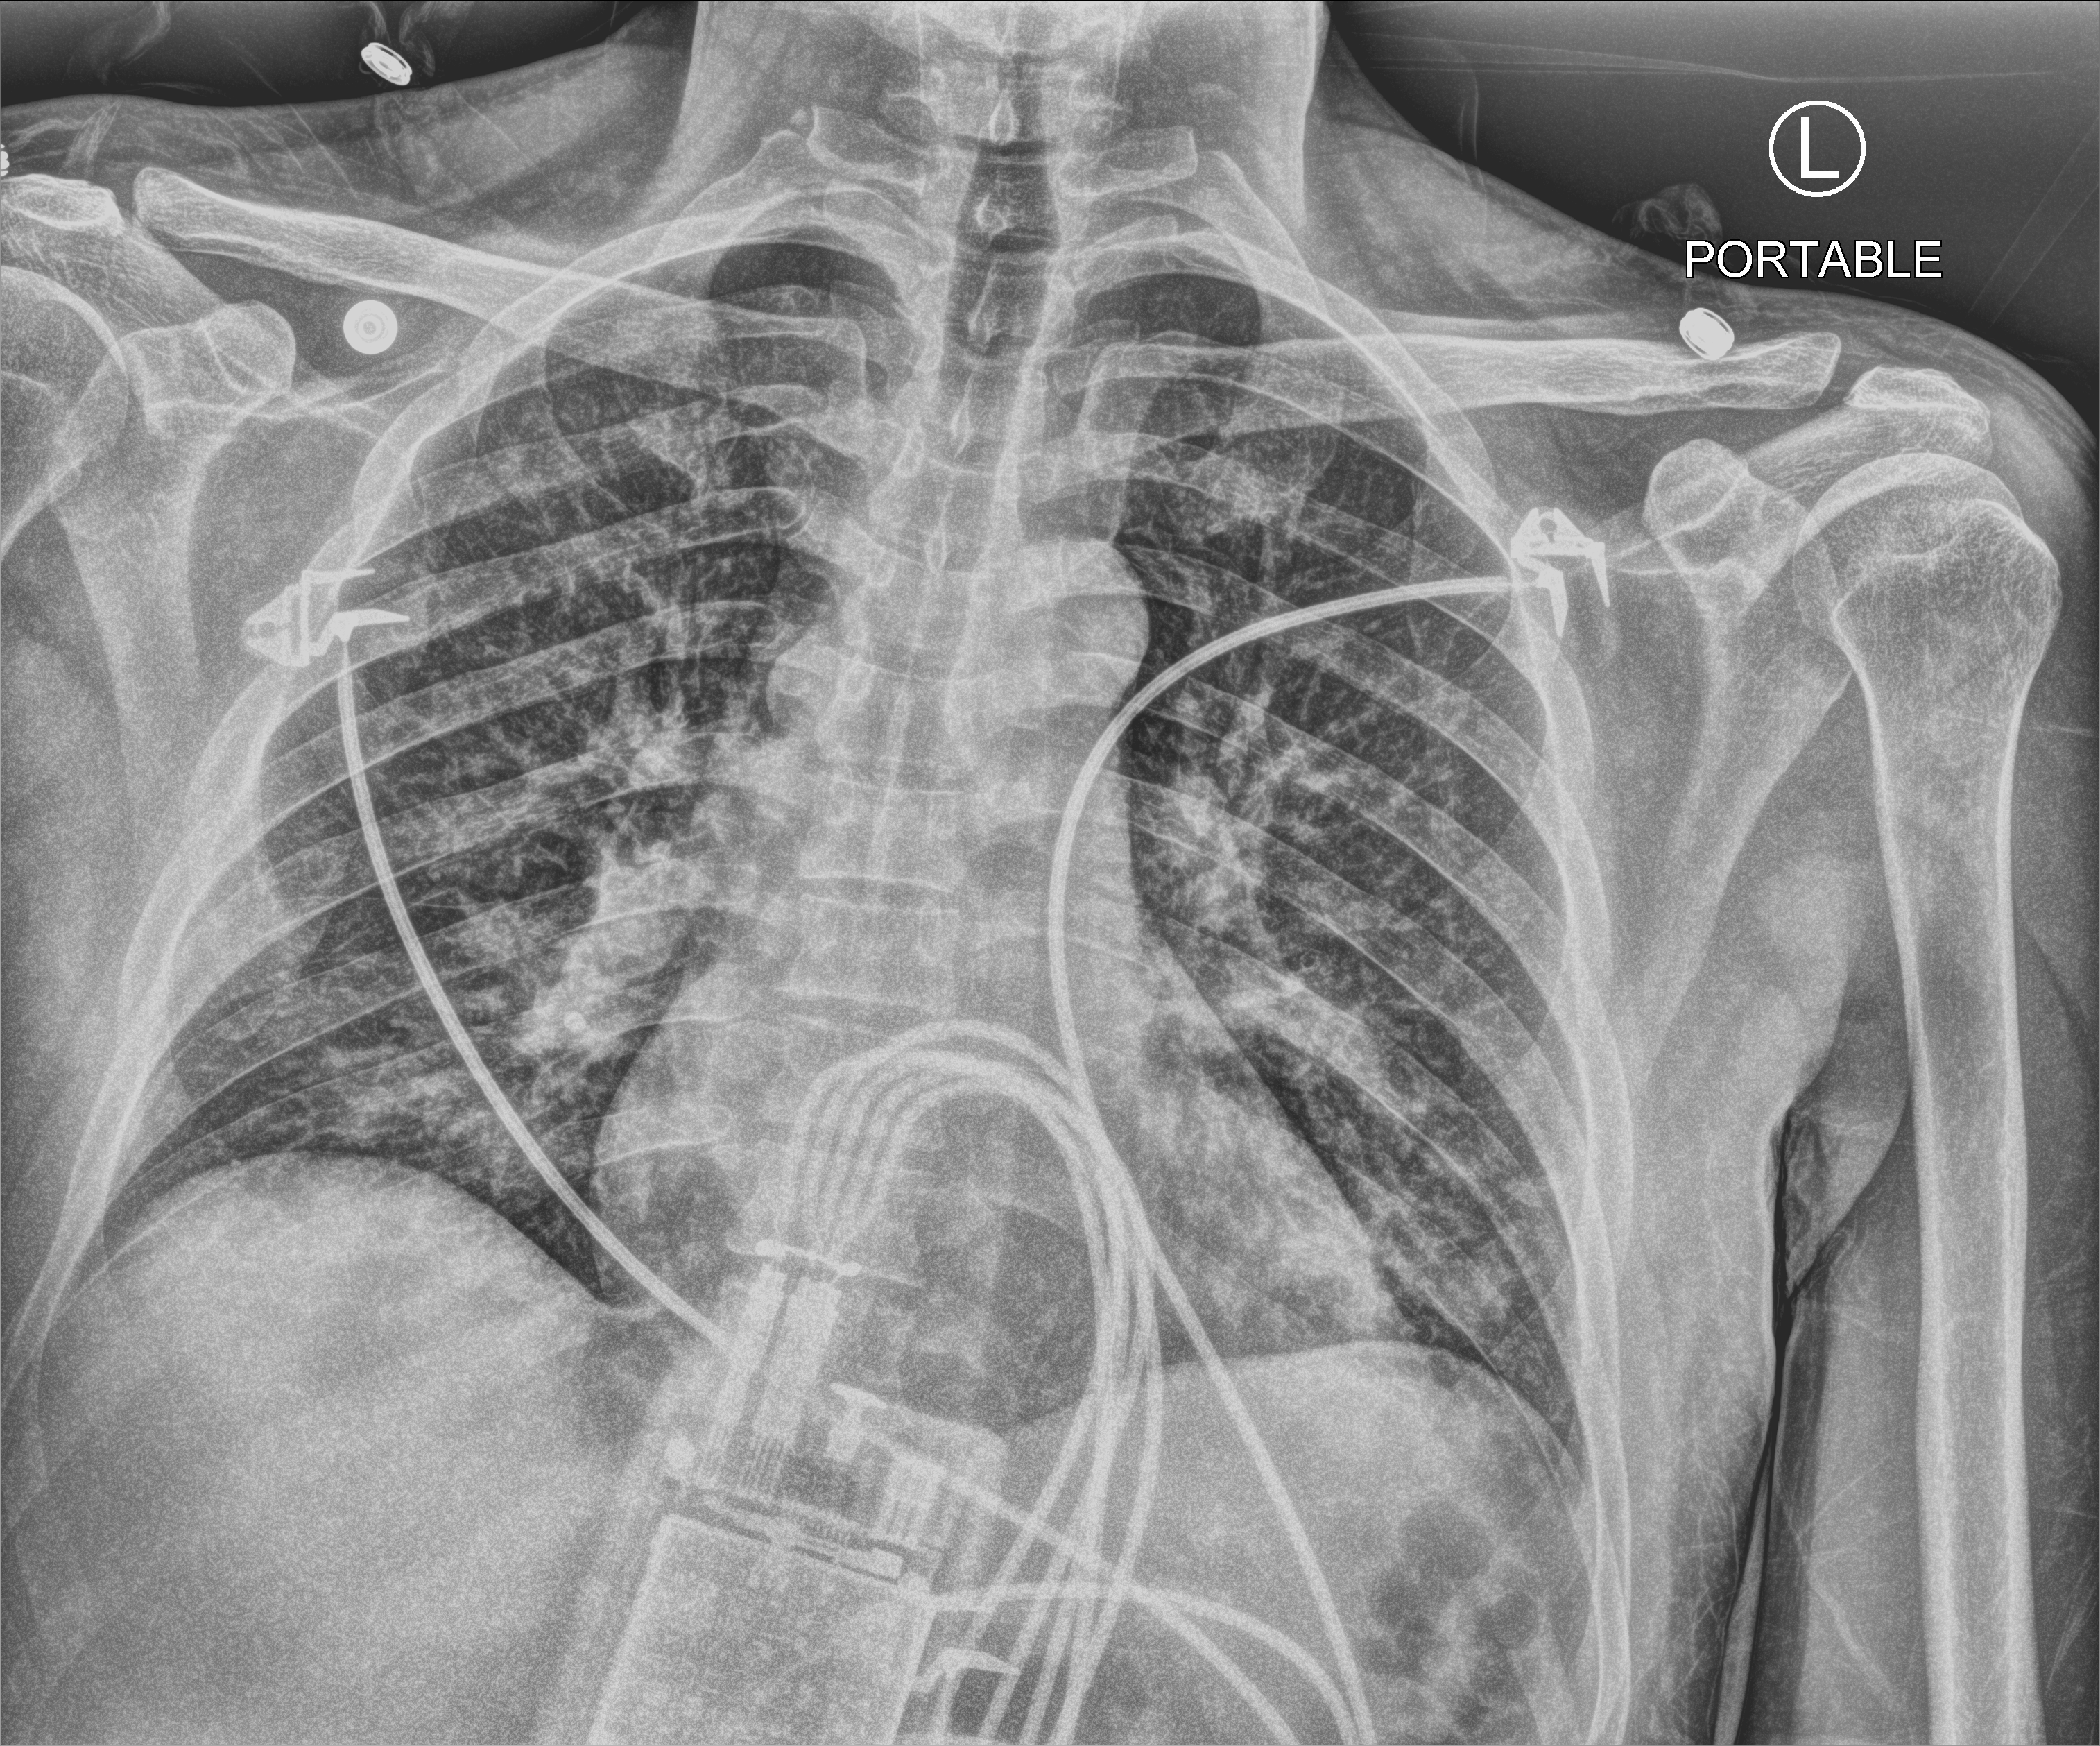
Portable chest radiograph, anteroposterior (AP) projection. Patient hospitalised with COVID-19; male, aged 18–59 years.
From the hospital-stay record, not from the radiograph (when in the stay this image was taken is not recorded): admitted to intensive care during this hospital stay: no.